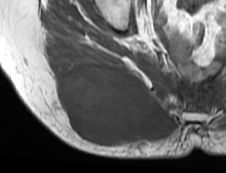
MRI of an extremity soft-tissue mass, one axial slice. Position 38 of 73 along the scan axis. MR volume resampled by the dataset authors to the PET/CT grid (not the native acquisition matrix). 3.27 mm slice thickness. 226 × 173 image matrix, field of view 221 × 169 mm. Female patient. From the clinical record (not read from this slice): histological type: spindle cell suggestive of myxofibrosarcoma; grade: intermediate; site of the primary tumour: right buttock.
Structures marked on this image (expert contour drawn on MRI and transferred to this co-registered scan by the dataset authors):
- gross tumour volume (mass): bounding box (x1, y1, x2, y2) in pixels: (56, 60, 174, 144)